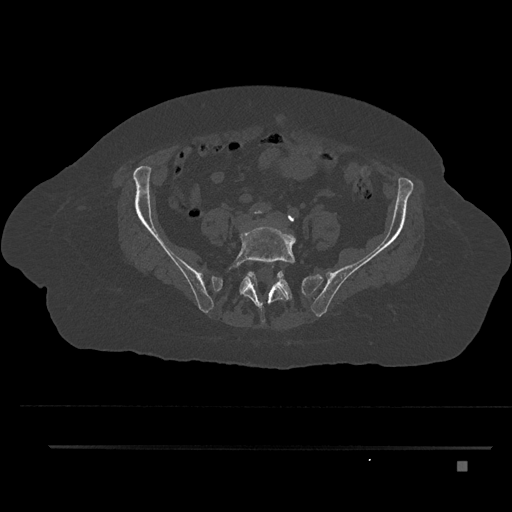
CT including the spine, one axial slice; position 34 of 797 along the scan axis; reconstruction kernel Br40s/3; 120 kVp; bone window (W 1800 / L 400 HU); 0.5 mm slice thickness; 512 × 512 image matrix, field of view 437 × 437 mm. Patient: female, 76 years. Case-level facts recorded for this patient, not image findings: primary cancer: lung; vertebrae with lytic lesions (as recorded): T11, L3.
Outlined on this slice (semi-automatically segmented with operator editing):
- L5 vertebra: bounding box [x1, y1, x2, y2] px = [231, 225, 296, 324]